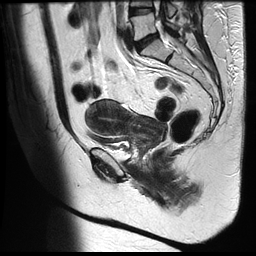
Pelvic MRI for cervical cancer, one sagittal slice. Slice 14 of 35 in the series (ordered by position). T2-weighted. 1.5 T. TE 122.8 ms, TR 4992 ms. 4 mm slice thickness. 256 × 256 image matrix, field of view 300 × 300 mm. Patient: female, 42 years.
Outlined on this slice (expert manual segmentation):
- uterus and cervix: bounding box [x1, y1, x2, y2] px = [85, 99, 164, 148]